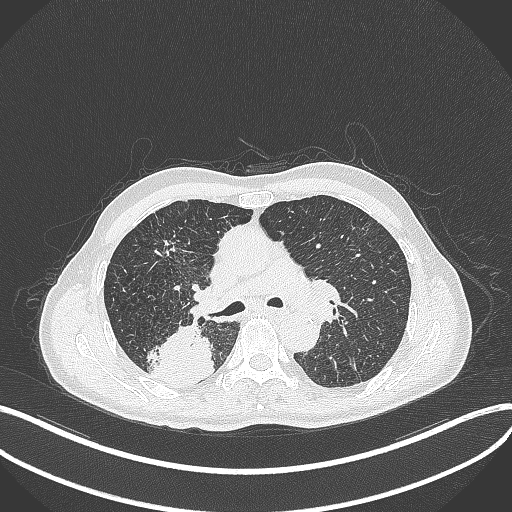
Chest CT, one axial slice; 120 kVp; lung window (W 1500 / L -600 HU); 512 × 512 image matrix, field of view 400 × 400 mm. Male patient, age 79 years. From the clinical record (not read from this slice): clinical TNM (as recorded): T3 N0 M0.
Outlined on this slice (rectangle marked by the reading radiologist):
- lung tumour (recorded histology: adenocarcinoma): bounding box [x1, y1, x2, y2] px = [150, 321, 216, 387]